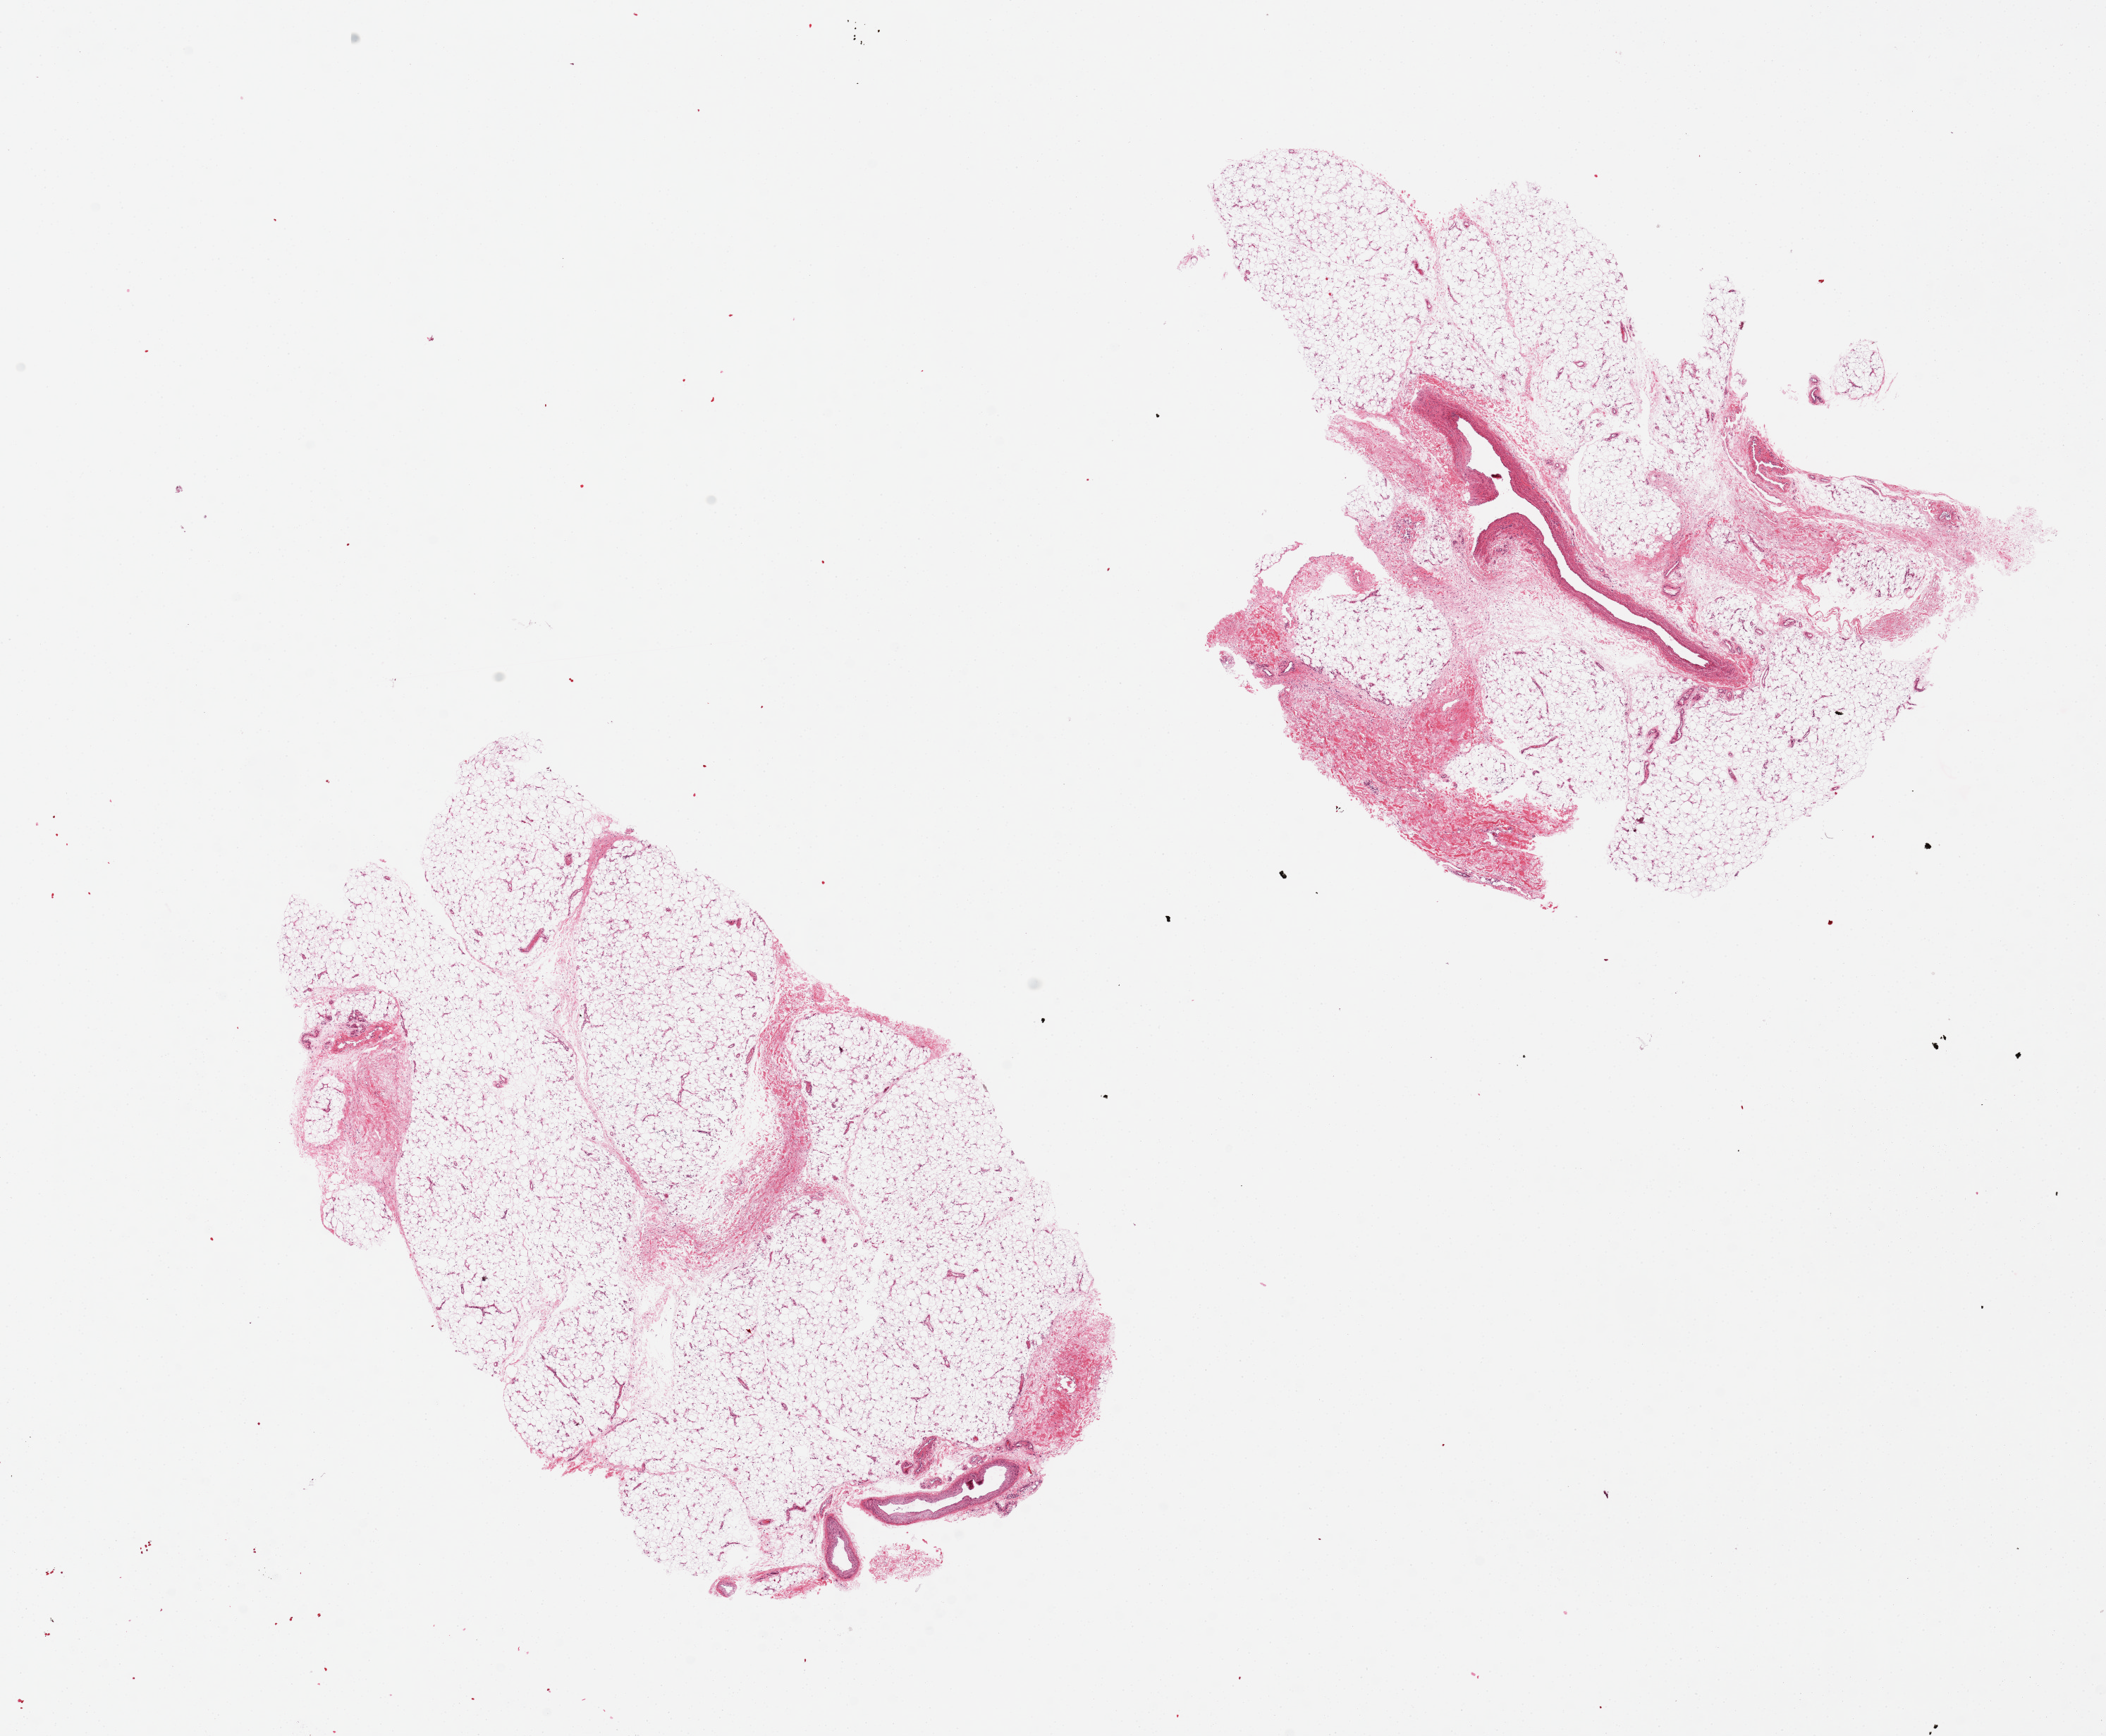
H&E whole-slide image, low-resolution overview of the scanned area, about 23.6 x 19.5 mm (from a 20x scan), PAXgene-fixed paraffin-embedded (PFPE) section, section of adipose tissue (target tissue), tissue donor sample. Donor sex: female.
* reviewer comment on this tissue sample: 2 pieces, ~15% vessel stroma